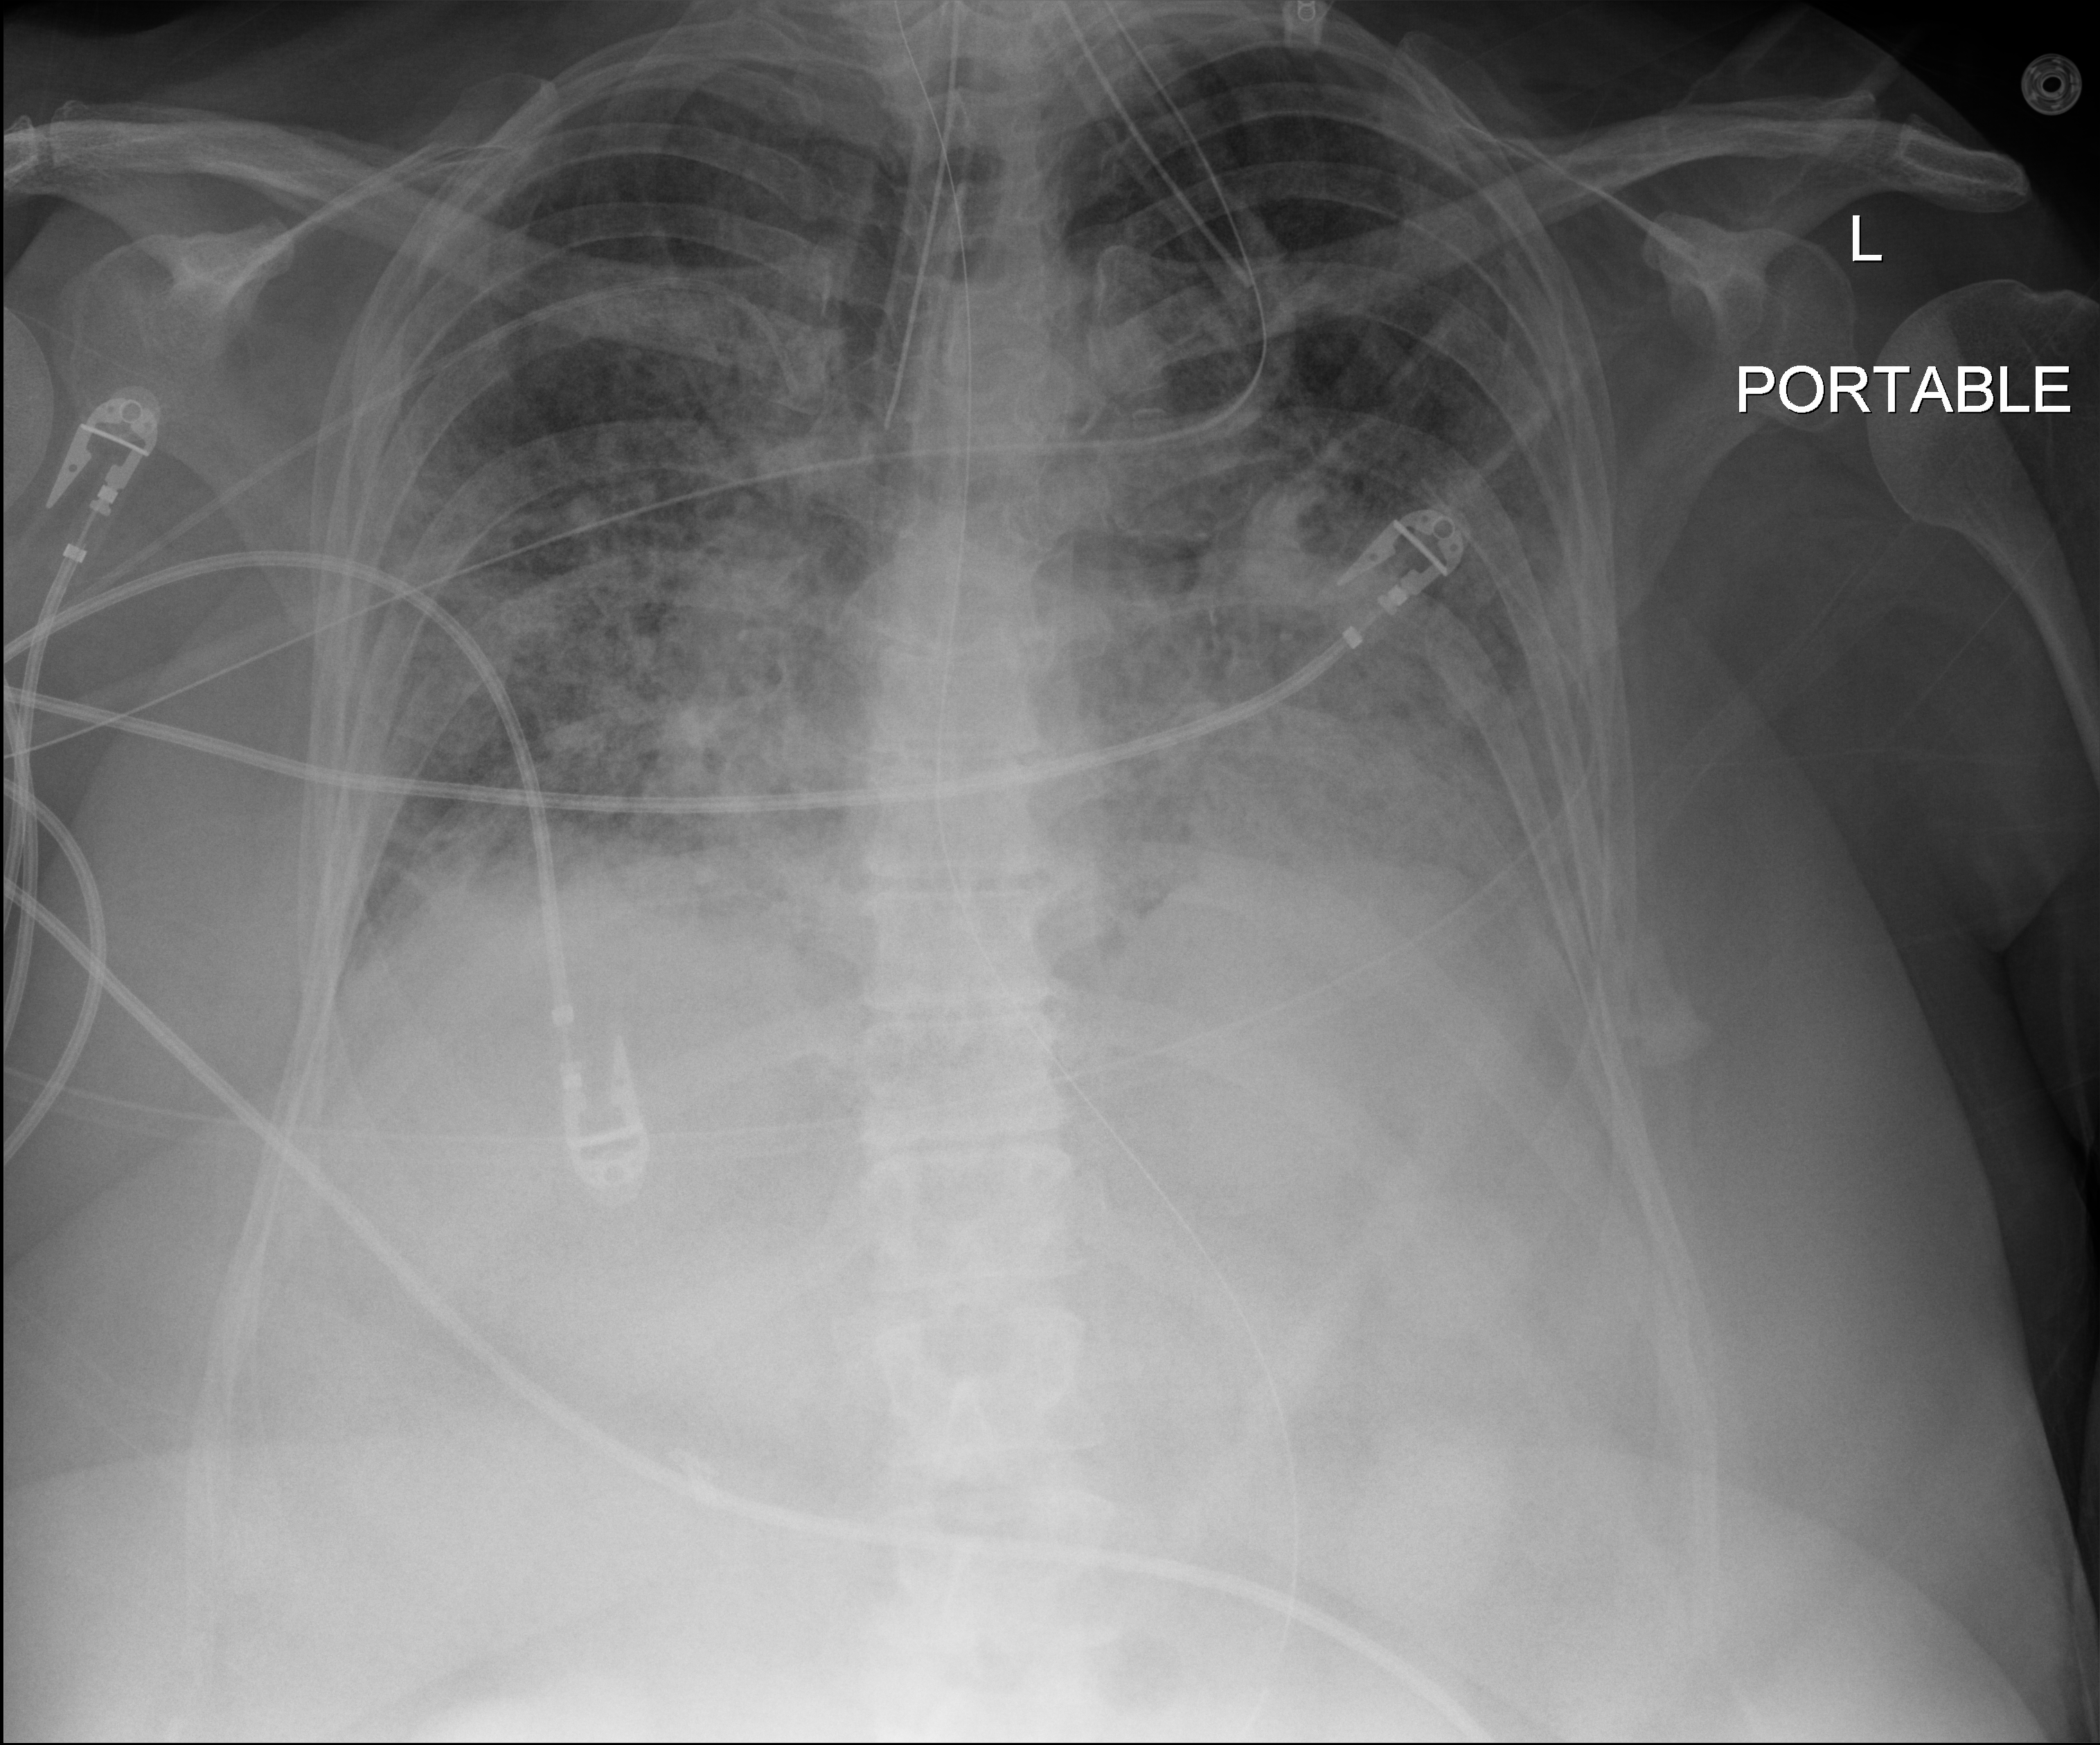
Portable chest radiograph; anteroposterior (AP) projection. Female patient hospitalised with COVID-19, age 60–74 years.
From the hospital-stay record, not from the radiograph (when in the stay this image was taken is not recorded): length of hospital stay: 45 days.